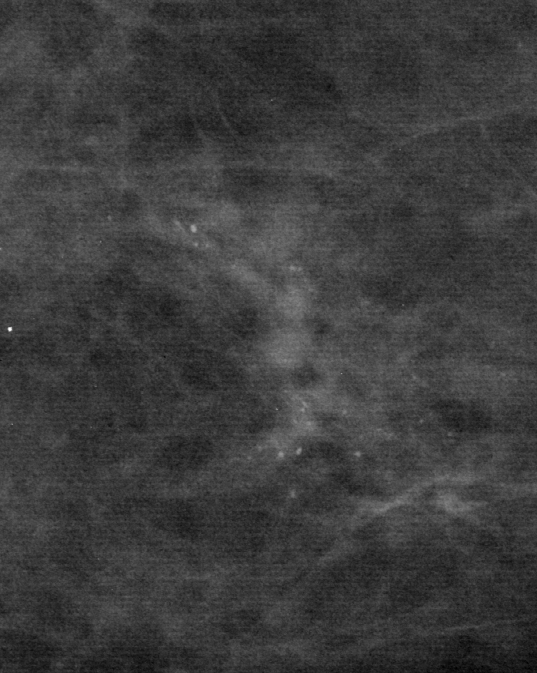
Cropped region of a digitized screen-film mammogram centred on a radiologist-marked abnormality, left breast, CC view, BI-RADS breast density category 2 (scale 1–4).
Calcifications, morphology pleomorphic, distribution clustered; BI-RADS assessment category 4; subtlety rating 2 on a 1 (subtle) to 5 (obvious) scale; pathology (as recorded): malignant.